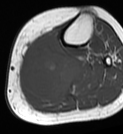
MRI of an extremity soft-tissue mass, one axial slice; slice 33 of 68 in the series (ordered by position); MR volume resampled by the dataset authors to the PET/CT grid (not the native acquisition matrix); 3.27 mm slice thickness; 123 × 134 image matrix, field of view 120 × 131 mm. Female patient. Case-level facts recorded for this patient, not image findings: histological type: extraskeletal high grade osteogenic sarcoma; grade: high; site of the primary tumour: left calf.
Outlined on this slice (expert contour drawn on MRI and transferred to this co-registered scan by the dataset authors):
- gross tumour volume (mass): box from (x=20, y=34) to (x=80, y=101) px